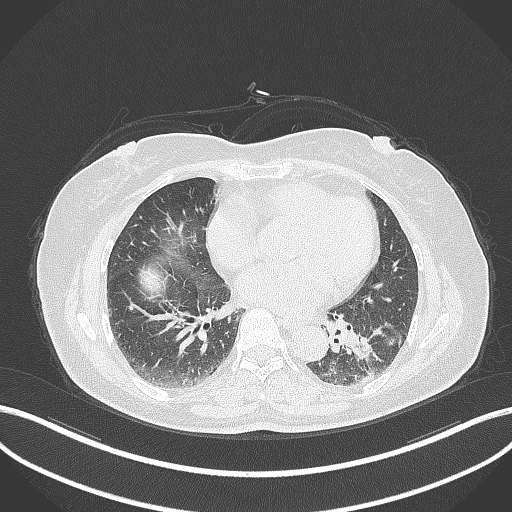
Chest CT, one axial slice; lung window (W 1500 / L -600 HU); 1 mm slice thickness; 512 × 512 image matrix, field of view 400 × 400 mm. Patient: female, 59 years. From the clinical record (not read from this slice): clinical TNM (as recorded): T2a N0 M0; histopathological grade: G2-3.
Annotated regions visible in this slice (bounding box drawn by a radiologist):
- lung tumour (recorded histology: adenocarcinoma): bounding box (x1, y1, x2, y2) in pixels: (339, 323, 384, 366)